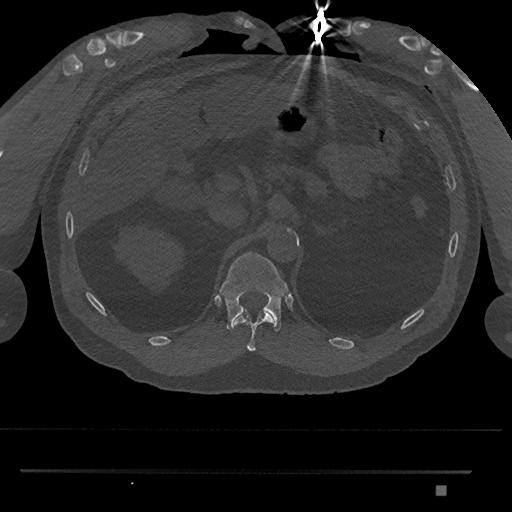
CT including the spine, one axial slice; position 909 of 1134 along the scan axis; reconstruction kernel Br40s/3; bone window (W 1800 / L 400 HU); 0.5 mm slice thickness; 512 × 512 image matrix, field of view 429 × 429 mm. Male patient, age 65 years. From the clinical record (not read from this slice): primary cancer: prostate.
Annotated regions visible in this slice (semi-automatically segmented with operator editing):
- T11 vertebra: bounding box <234,310,273,352> (left, top, right, bottom; pixels)
- T12 vertebra: <219,252,289,332>